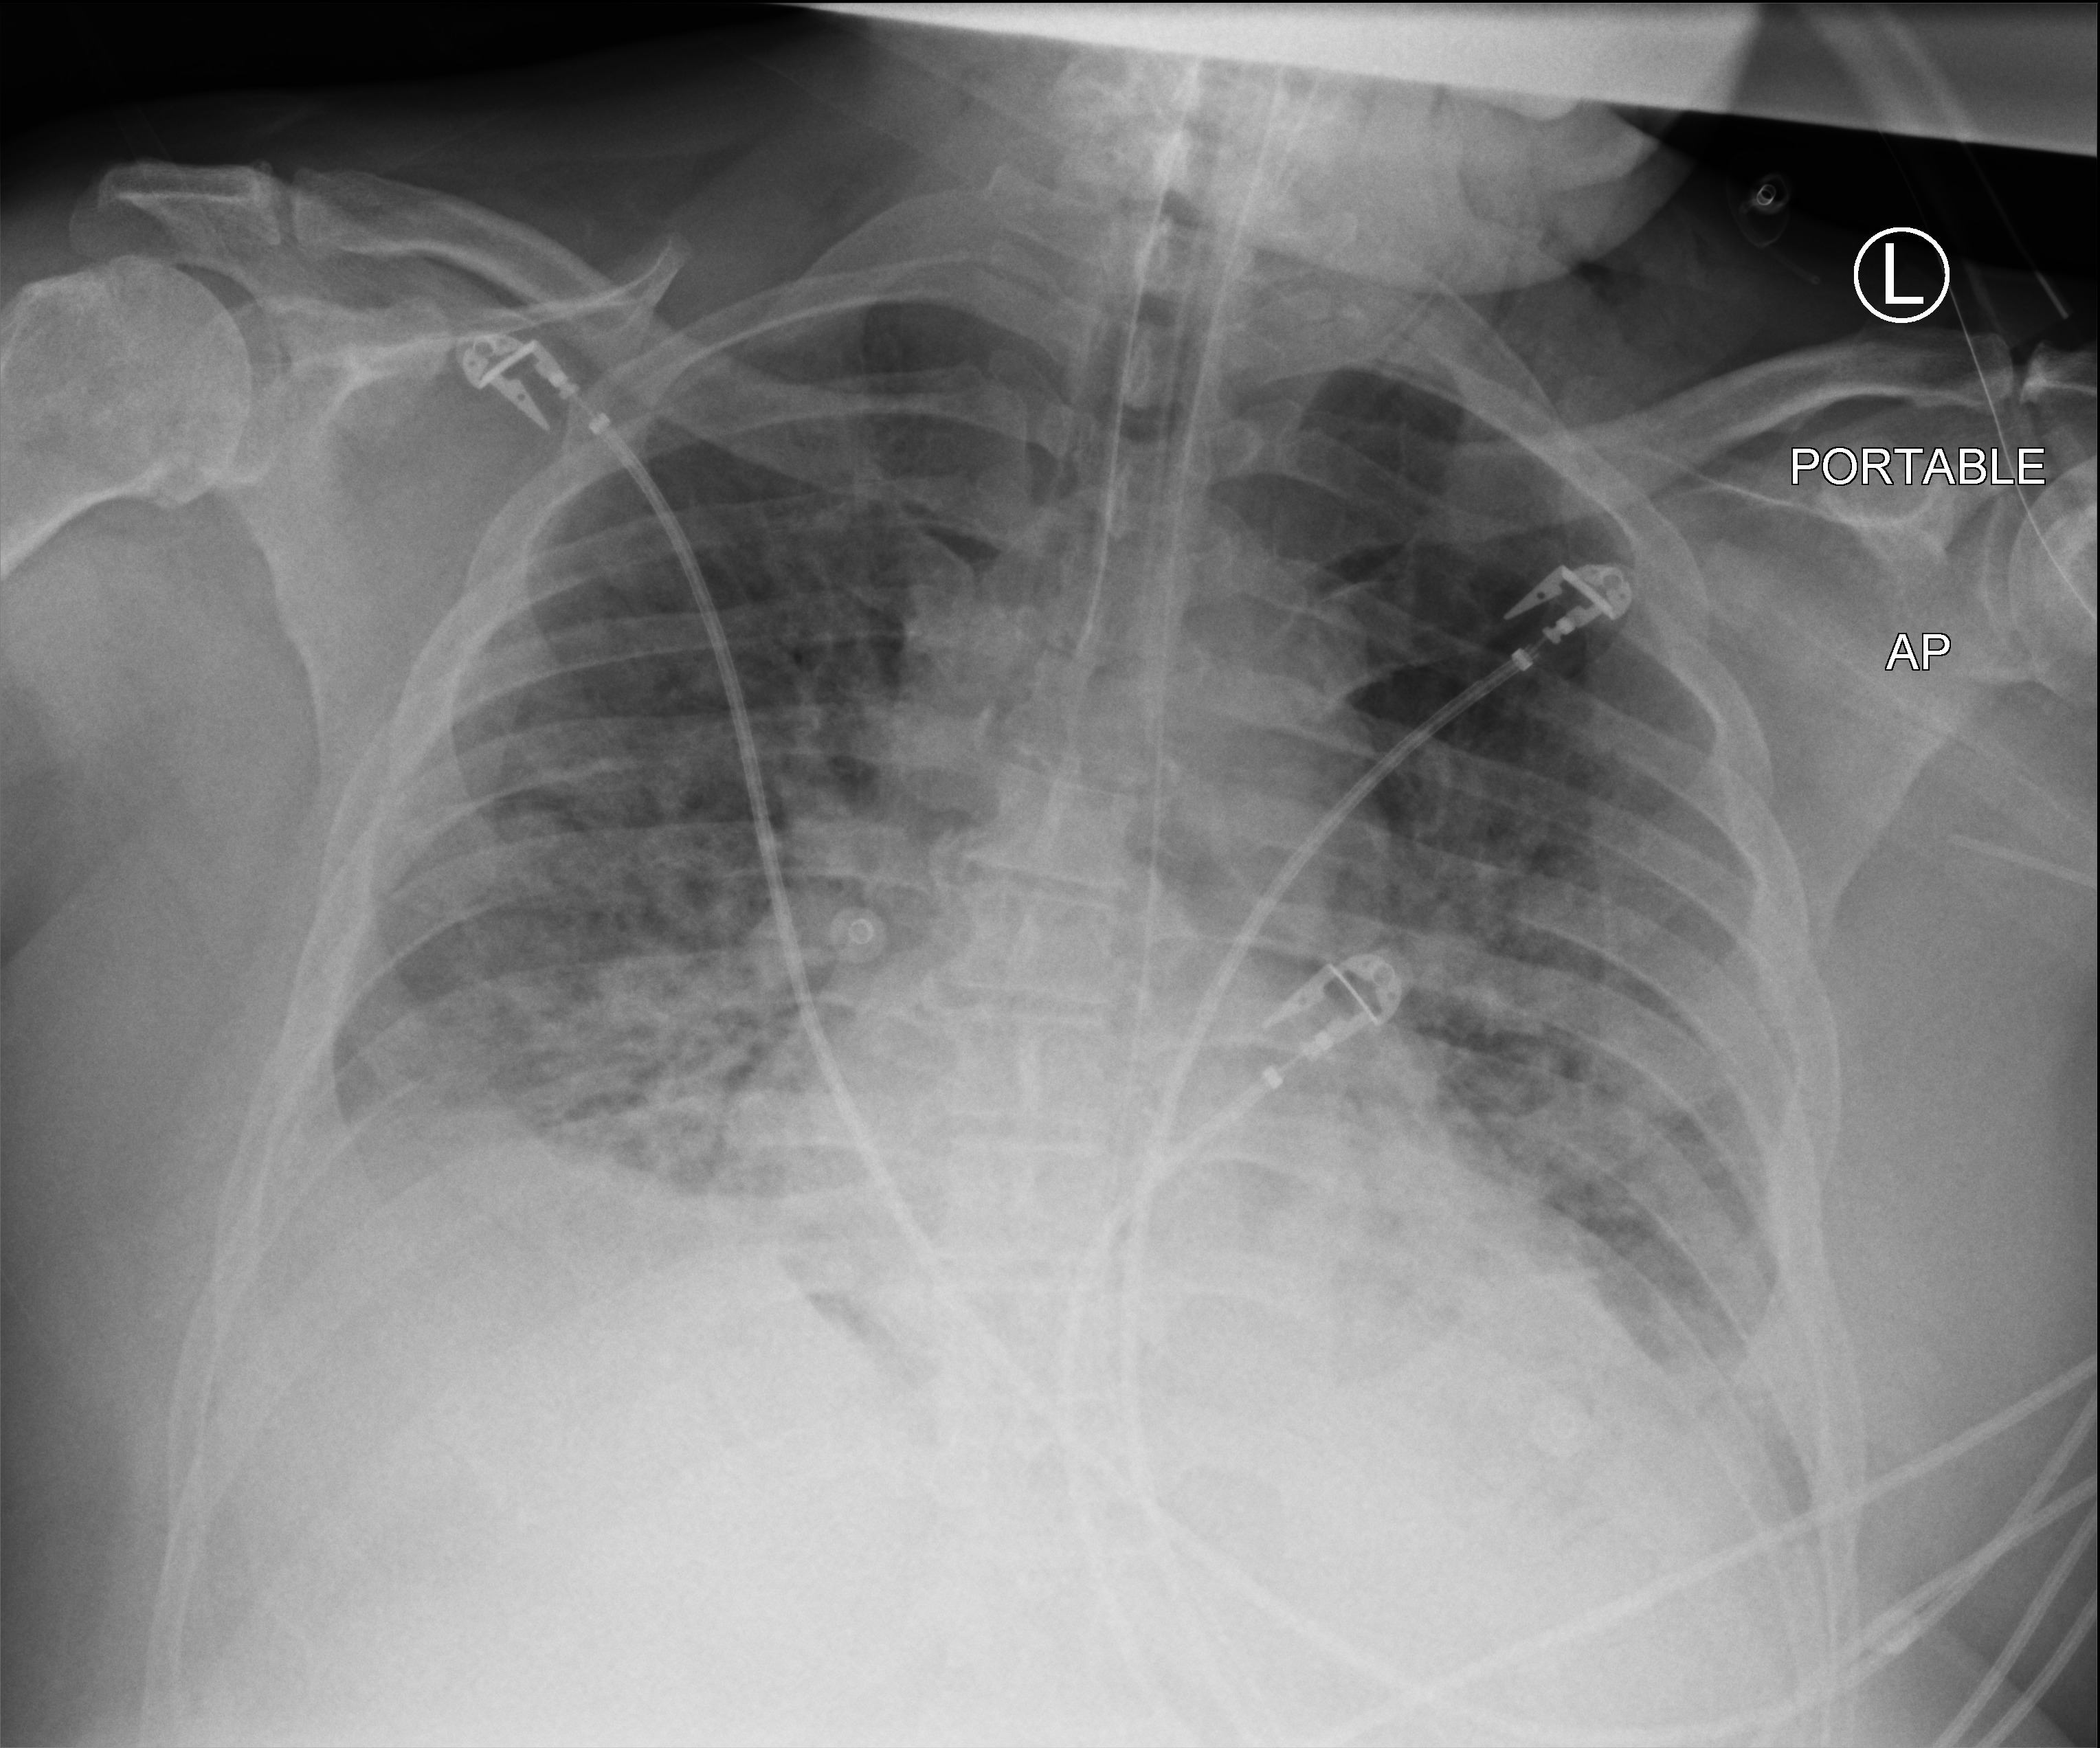
Portable chest radiograph; anteroposterior (AP) projection. Patient hospitalised with COVID-19; male, aged 18–59 years.
Hospital-stay facts (about this admission, not read from this image; timing relative to this image not recorded): mechanically ventilated during this hospital stay: yes.